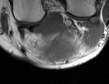
MRI of an extremity soft-tissue mass, one axial slice. Slice 14 of 50 in the series (ordered by position). MR volume resampled by the dataset authors to the PET/CT grid (not the native acquisition matrix). 3.27 mm slice thickness. 109 × 84 image matrix, field of view 106 × 82 mm. Male patient. Case-level facts recorded for this patient, not image findings: histological type: synovial sarcoma; site of the primary tumour: left poplietal fossa.
Annotated regions visible in this slice (expert contour drawn on MRI and transferred to this co-registered scan by the dataset authors):
- gross tumour volume (mass): bounding box <39,37,76,61> (left, top, right, bottom; pixels)